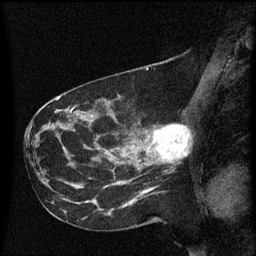
Breast MRI (dynamic contrast-enhanced), one sagittal slice. Slice 28 of 60 in the series (ordered by position). Dynamic contrast-enhanced series, image 2 of 3 at this slice position (ordered by acquisition). 1.5 T. TE 4.2 ms, TR 8.4 ms. 2 mm slice thickness. 256 × 256 image matrix, field of view 200 × 200 mm. Patient: female, 41 years. Case-level facts recorded for this patient, not image findings: setting: breast cancer imaged before/during neoadjuvant chemotherapy; receptor status: triple-negative.
Structures marked on this image (semi-automatic segmentation, software-assisted and operator-edited):
- analysis volume of interest (the breast-tissue region the enhancement analysis was run in; not a lesion): bounding box (x1, y1, x2, y2) in pixels: (138, 124, 190, 173)
- tumour enhancement mask (voxels above the 70 % enhancement threshold inside the analysis volume of interest): (153, 124, 188, 159)